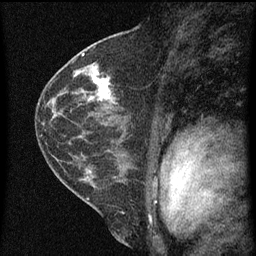
Breast MRI (dynamic contrast-enhanced), one sagittal slice. Position 35 of 60 along the scan axis. Dynamic contrast-enhanced series, image 2 of 3 at this slice position (ordered by acquisition). 1.5 T. TE 4.2 ms, TR 8 ms. 2 mm slice thickness. 256 × 256 image matrix. Patient: female, 48 years.
Annotated regions visible in this slice (semi-automatically segmented with operator editing):
- analysis volume of interest (the breast-tissue region the enhancement analysis was run in; not a lesion): bounding box [x1, y1, x2, y2] px = [82, 68, 126, 125]
- tumour enhancement mask (voxels above the 70 % enhancement threshold inside the analysis volume of interest): [86, 70, 115, 103]